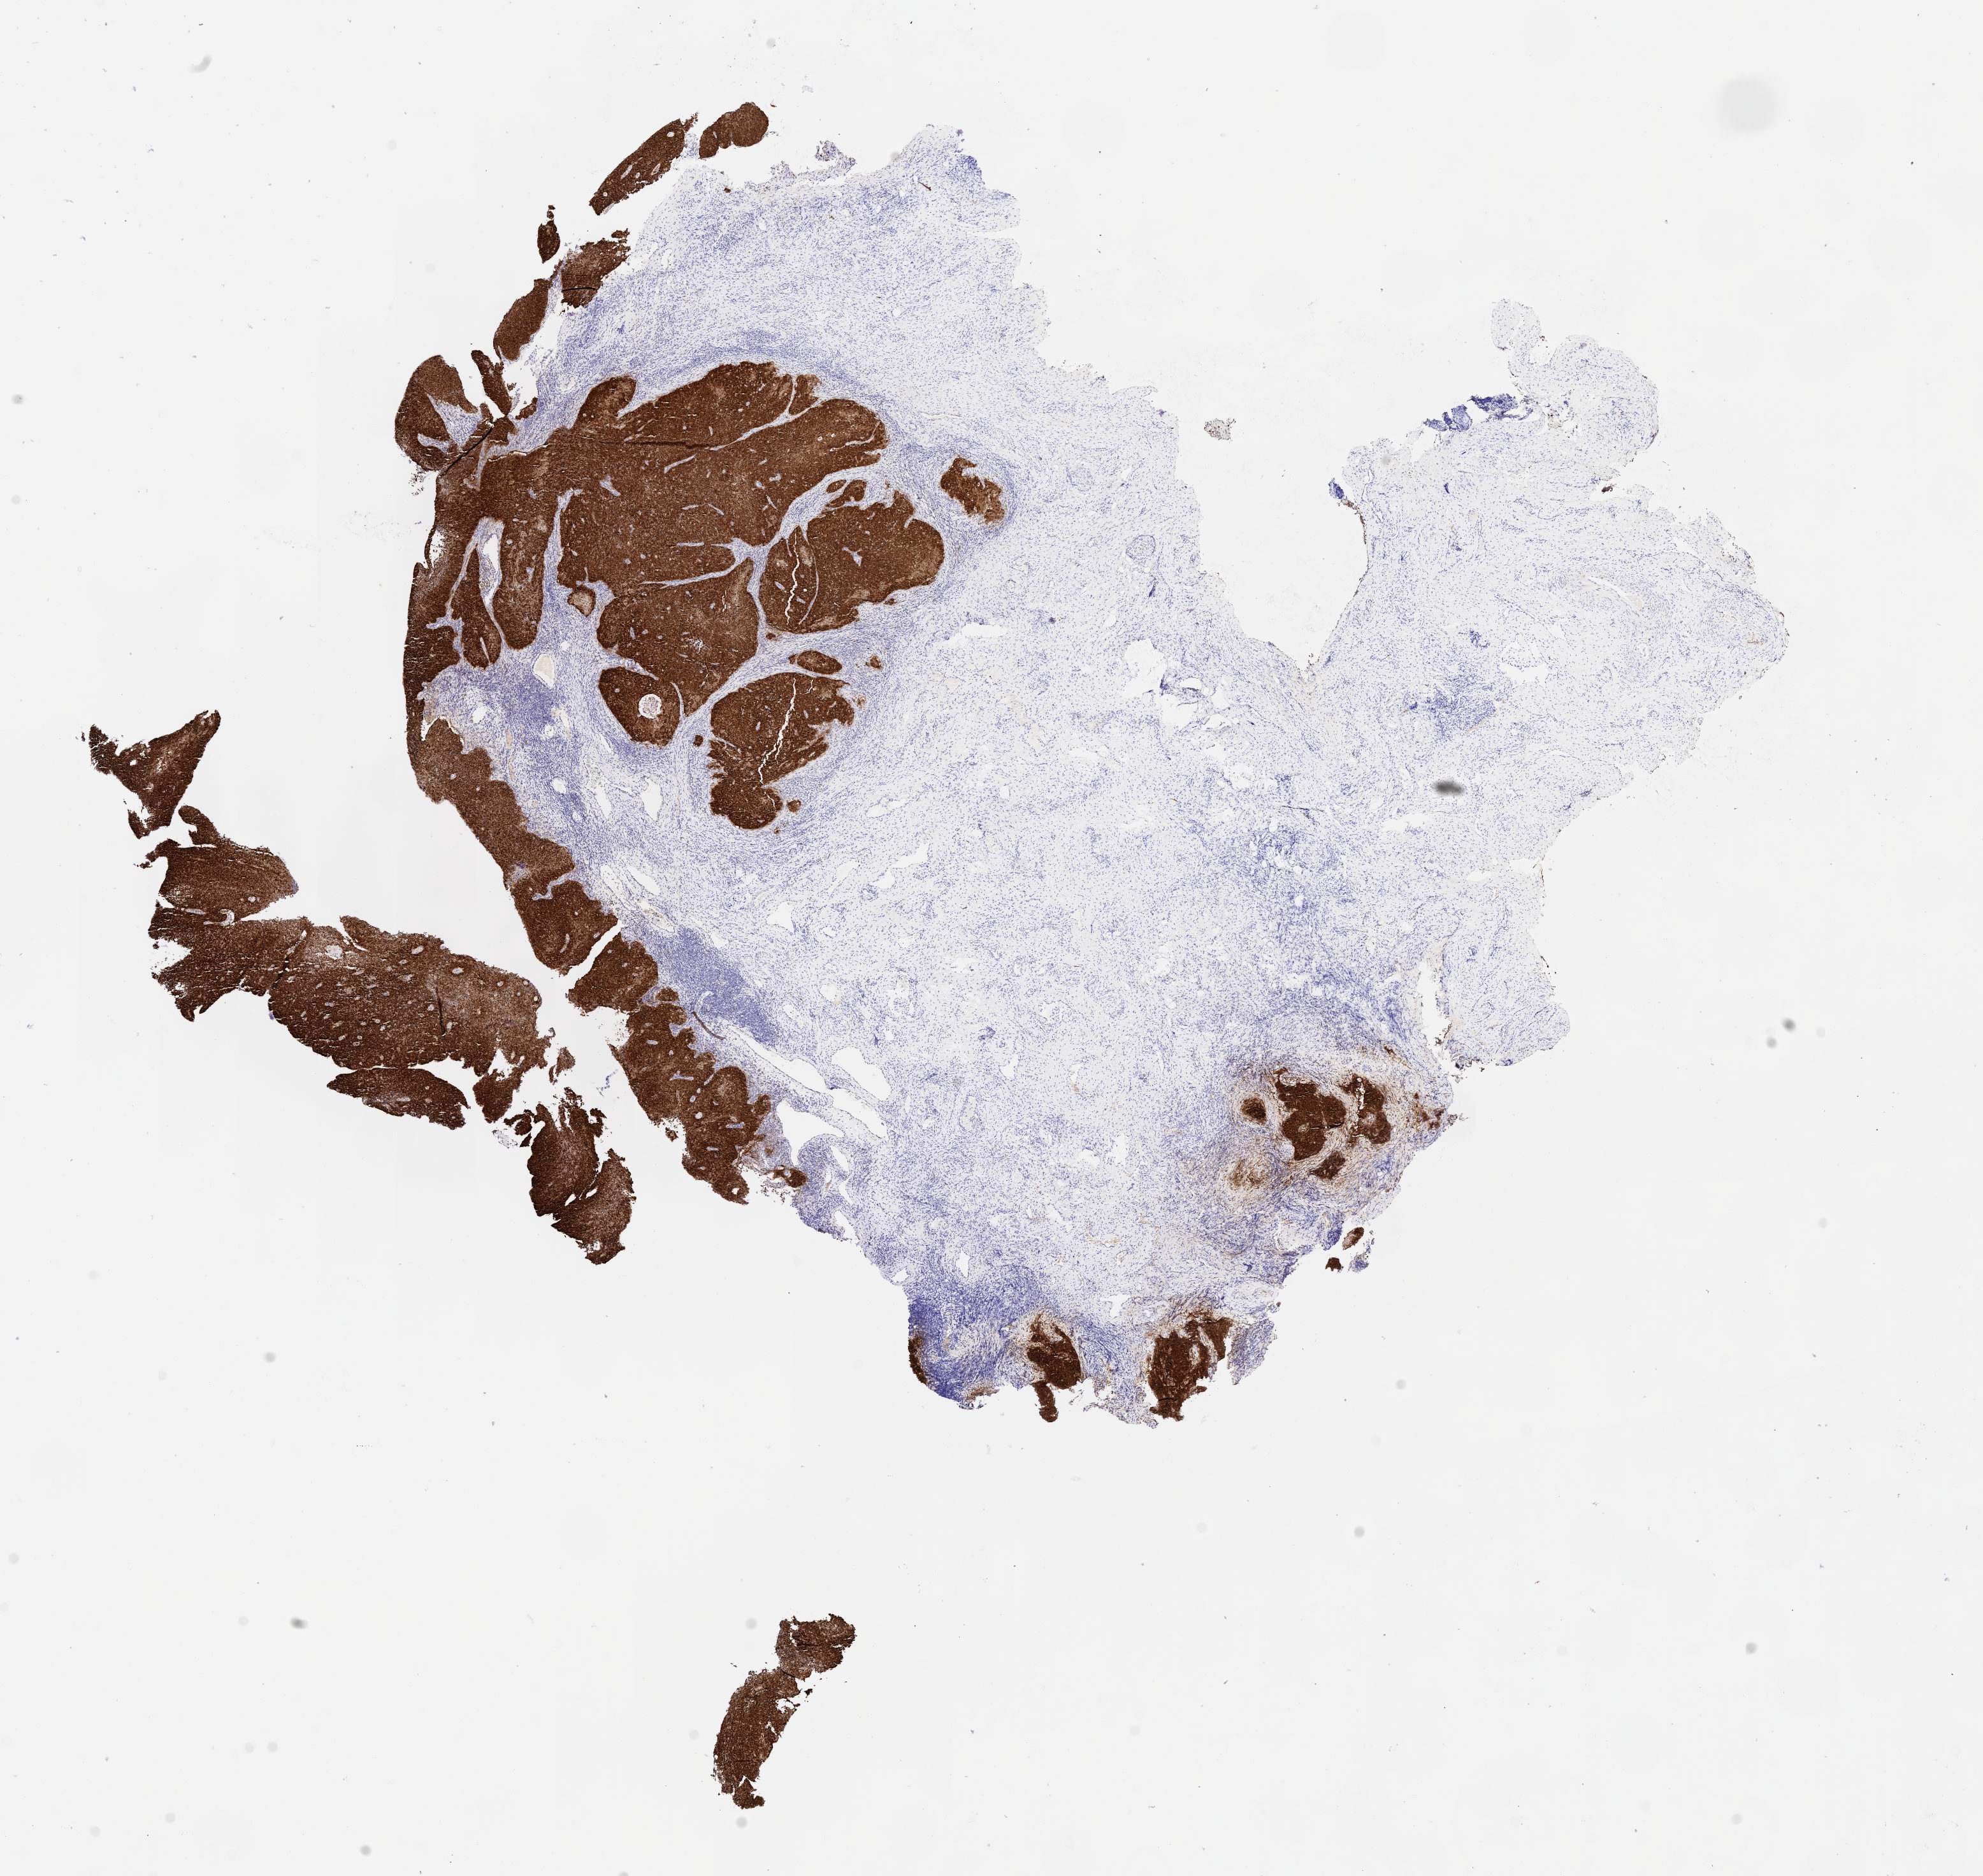
Whole-slide image, immunohistochemical stain for p16 (p16INK4a), a low-resolution overview of the entire scanned area, about 12.6 x 11.9 mm. Specimen: tumor tissue. Site: cervix. Female patient, 52 years old.
• diagnosis: Squamous cell carcinoma, large cell, nonkeratinizing, NOS